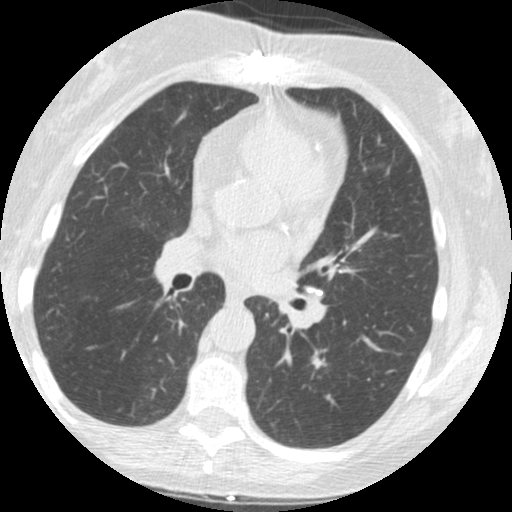
Chest CT (low-dose screening protocol), one axial image; baseline screening round; lung window (W 1500 / L -600 HU); standard (soft-tissue) reconstruction kernel (STANDARD); 120 kVp. Female participant, aged 61 years at enrolment.
• Lesion marked by an expert reader, bounding box <301,337,348,392> (left, top, right, bottom; pixels).
• Reader record for this screening exam (exam-level; its link to the box is not recorded): non-calcified nodule or mass ≥4 mm, left lower lobe, 12 × 11 mm, spiculated (stellate) margins, soft tissue attenuation.
• Lung cancer was diagnosed 440 days after this screen (after the second annual screen): squamous cell carcinoma, NOS, left lower lobe, moderately differentiated (G2), stage IA (AJCC 6th edition), 12 mm at pathology.